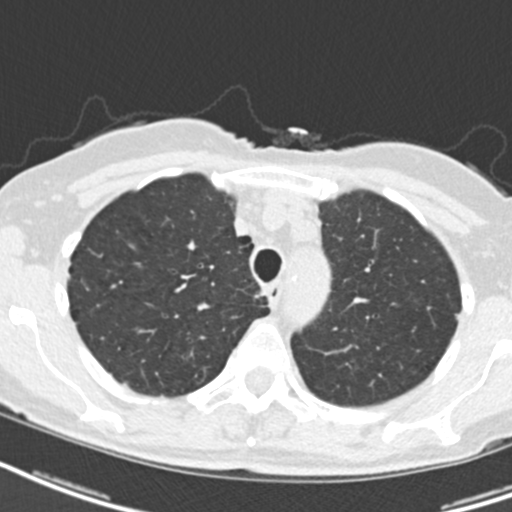
Low-dose screening chest CT, axial slice, baseline annual screen, lung window (W 1500 / L -600 HU), standard (soft-tissue) reconstruction kernel (B30f), 512 × 512 image matrix. Female, age 68 years at enrolment. Current smoker at enrolment.
• Expert reader's lesion annotation, bounding box [x1, y1, x2, y2] px = [248, 285, 272, 314].
• No non-calcified nodule or mass ≥4 mm was recorded by the screening reader at this exam.
• Official screen result: negative screen, no significant abnormalities.